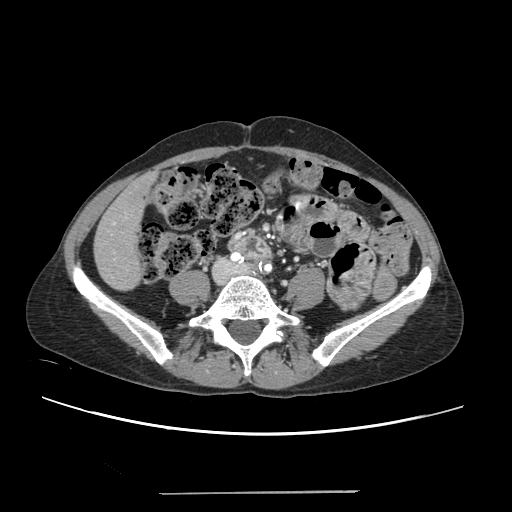
Contrast-enhanced abdominal CT, one axial slice; intravenous contrast given; soft-tissue window (W 400 / L 40 HU); 1.25 mm slice thickness; 512 × 512 image matrix. Female patient, age 60 years. Case-level facts recorded for this patient, not image findings: diagnosis: colorectal cancer liver metastases, imaged before liver resection; multiple liver metastases: no; largest metastasis: 1.5 cm.
Outlined on this slice (expert manual segmentation):
- liver: bounding box [x1, y1, x2, y2] px = [95, 176, 152, 290]
- planned liver remnant (the part of the liver to remain after resection): [95, 176, 152, 290]
- portal vein (with intrahepatic branches): [112, 217, 126, 259]